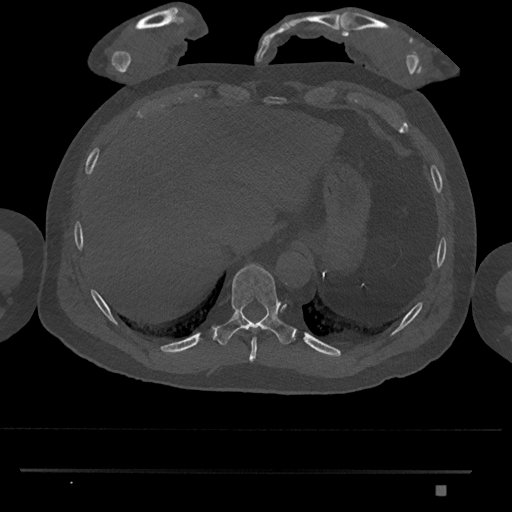
CT including the spine, one axial slice; bone window (W 1800 / L 400 HU); 512 × 512 image matrix, field of view 429 × 429 mm. Male patient, age 65 years. From the clinical record (not read from this slice): primary cancer: prostate.
Structures marked on this image (semi-automatic segmentation, software-assisted and operator-edited):
- T10 vertebra: bounding box <212,264,296,345> (left, top, right, bottom; pixels)
- T9 vertebra: <249,337,257,362>